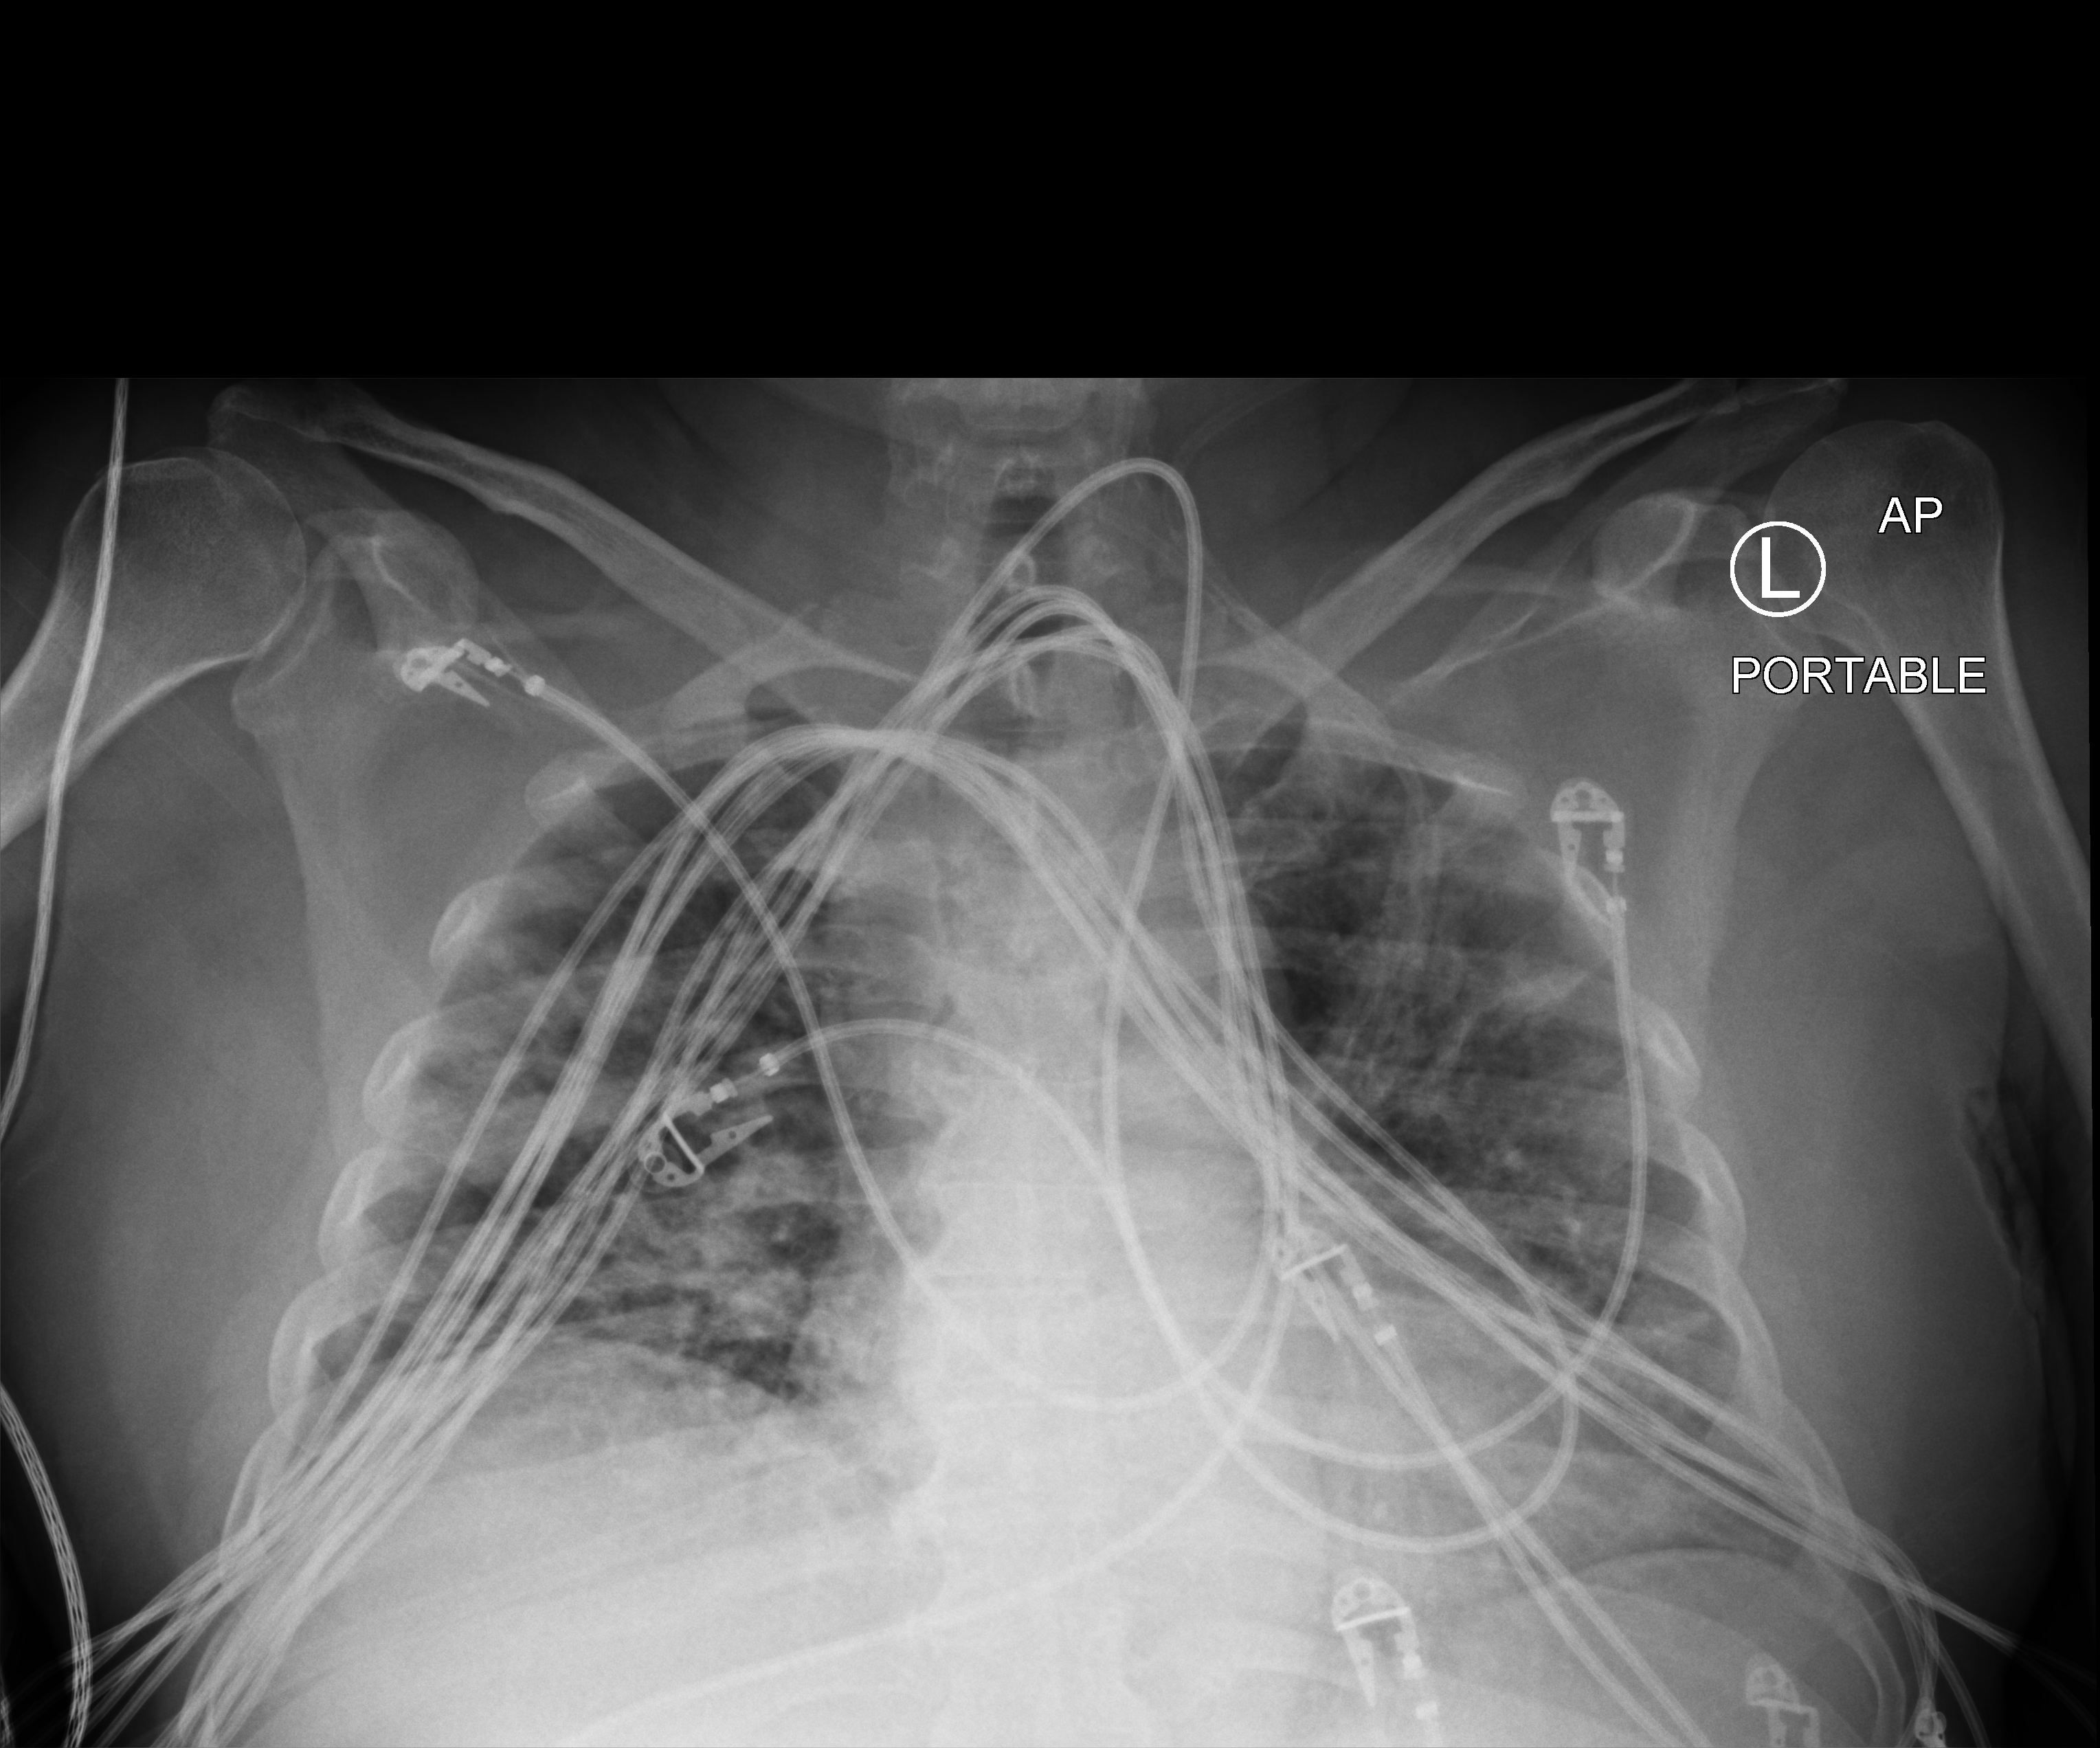
Chest X-ray (portable). Patient hospitalised with COVID-19; male, aged 18–59 years.
From the hospital-stay record, not from the radiograph (when in the stay this image was taken is not recorded): admitted to intensive care during this hospital stay: yes; mechanically ventilated during this hospital stay: yes; hypertension (admission record): yes.